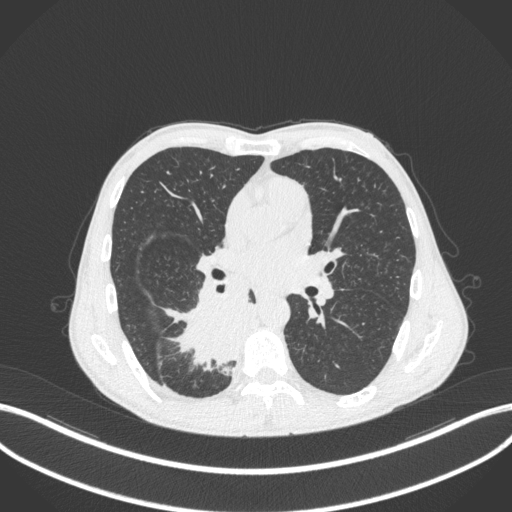
Chest CT, one axial slice; slice 196 of 371 in the series (ordered by position); lung window (W 1500 / L -600 HU); 1 mm slice thickness; 512 × 512 image matrix, field of view 400 × 400 mm. Patient: male, 58 years. Case-level facts recorded for this patient, not image findings: clinical TNM (as recorded): T3 N1 M1.
Outlined on this slice (bounding box drawn by a radiologist):
- lung tumour (recorded histology: squamous cell carcinoma): box from (x=155, y=289) to (x=265, y=374) px